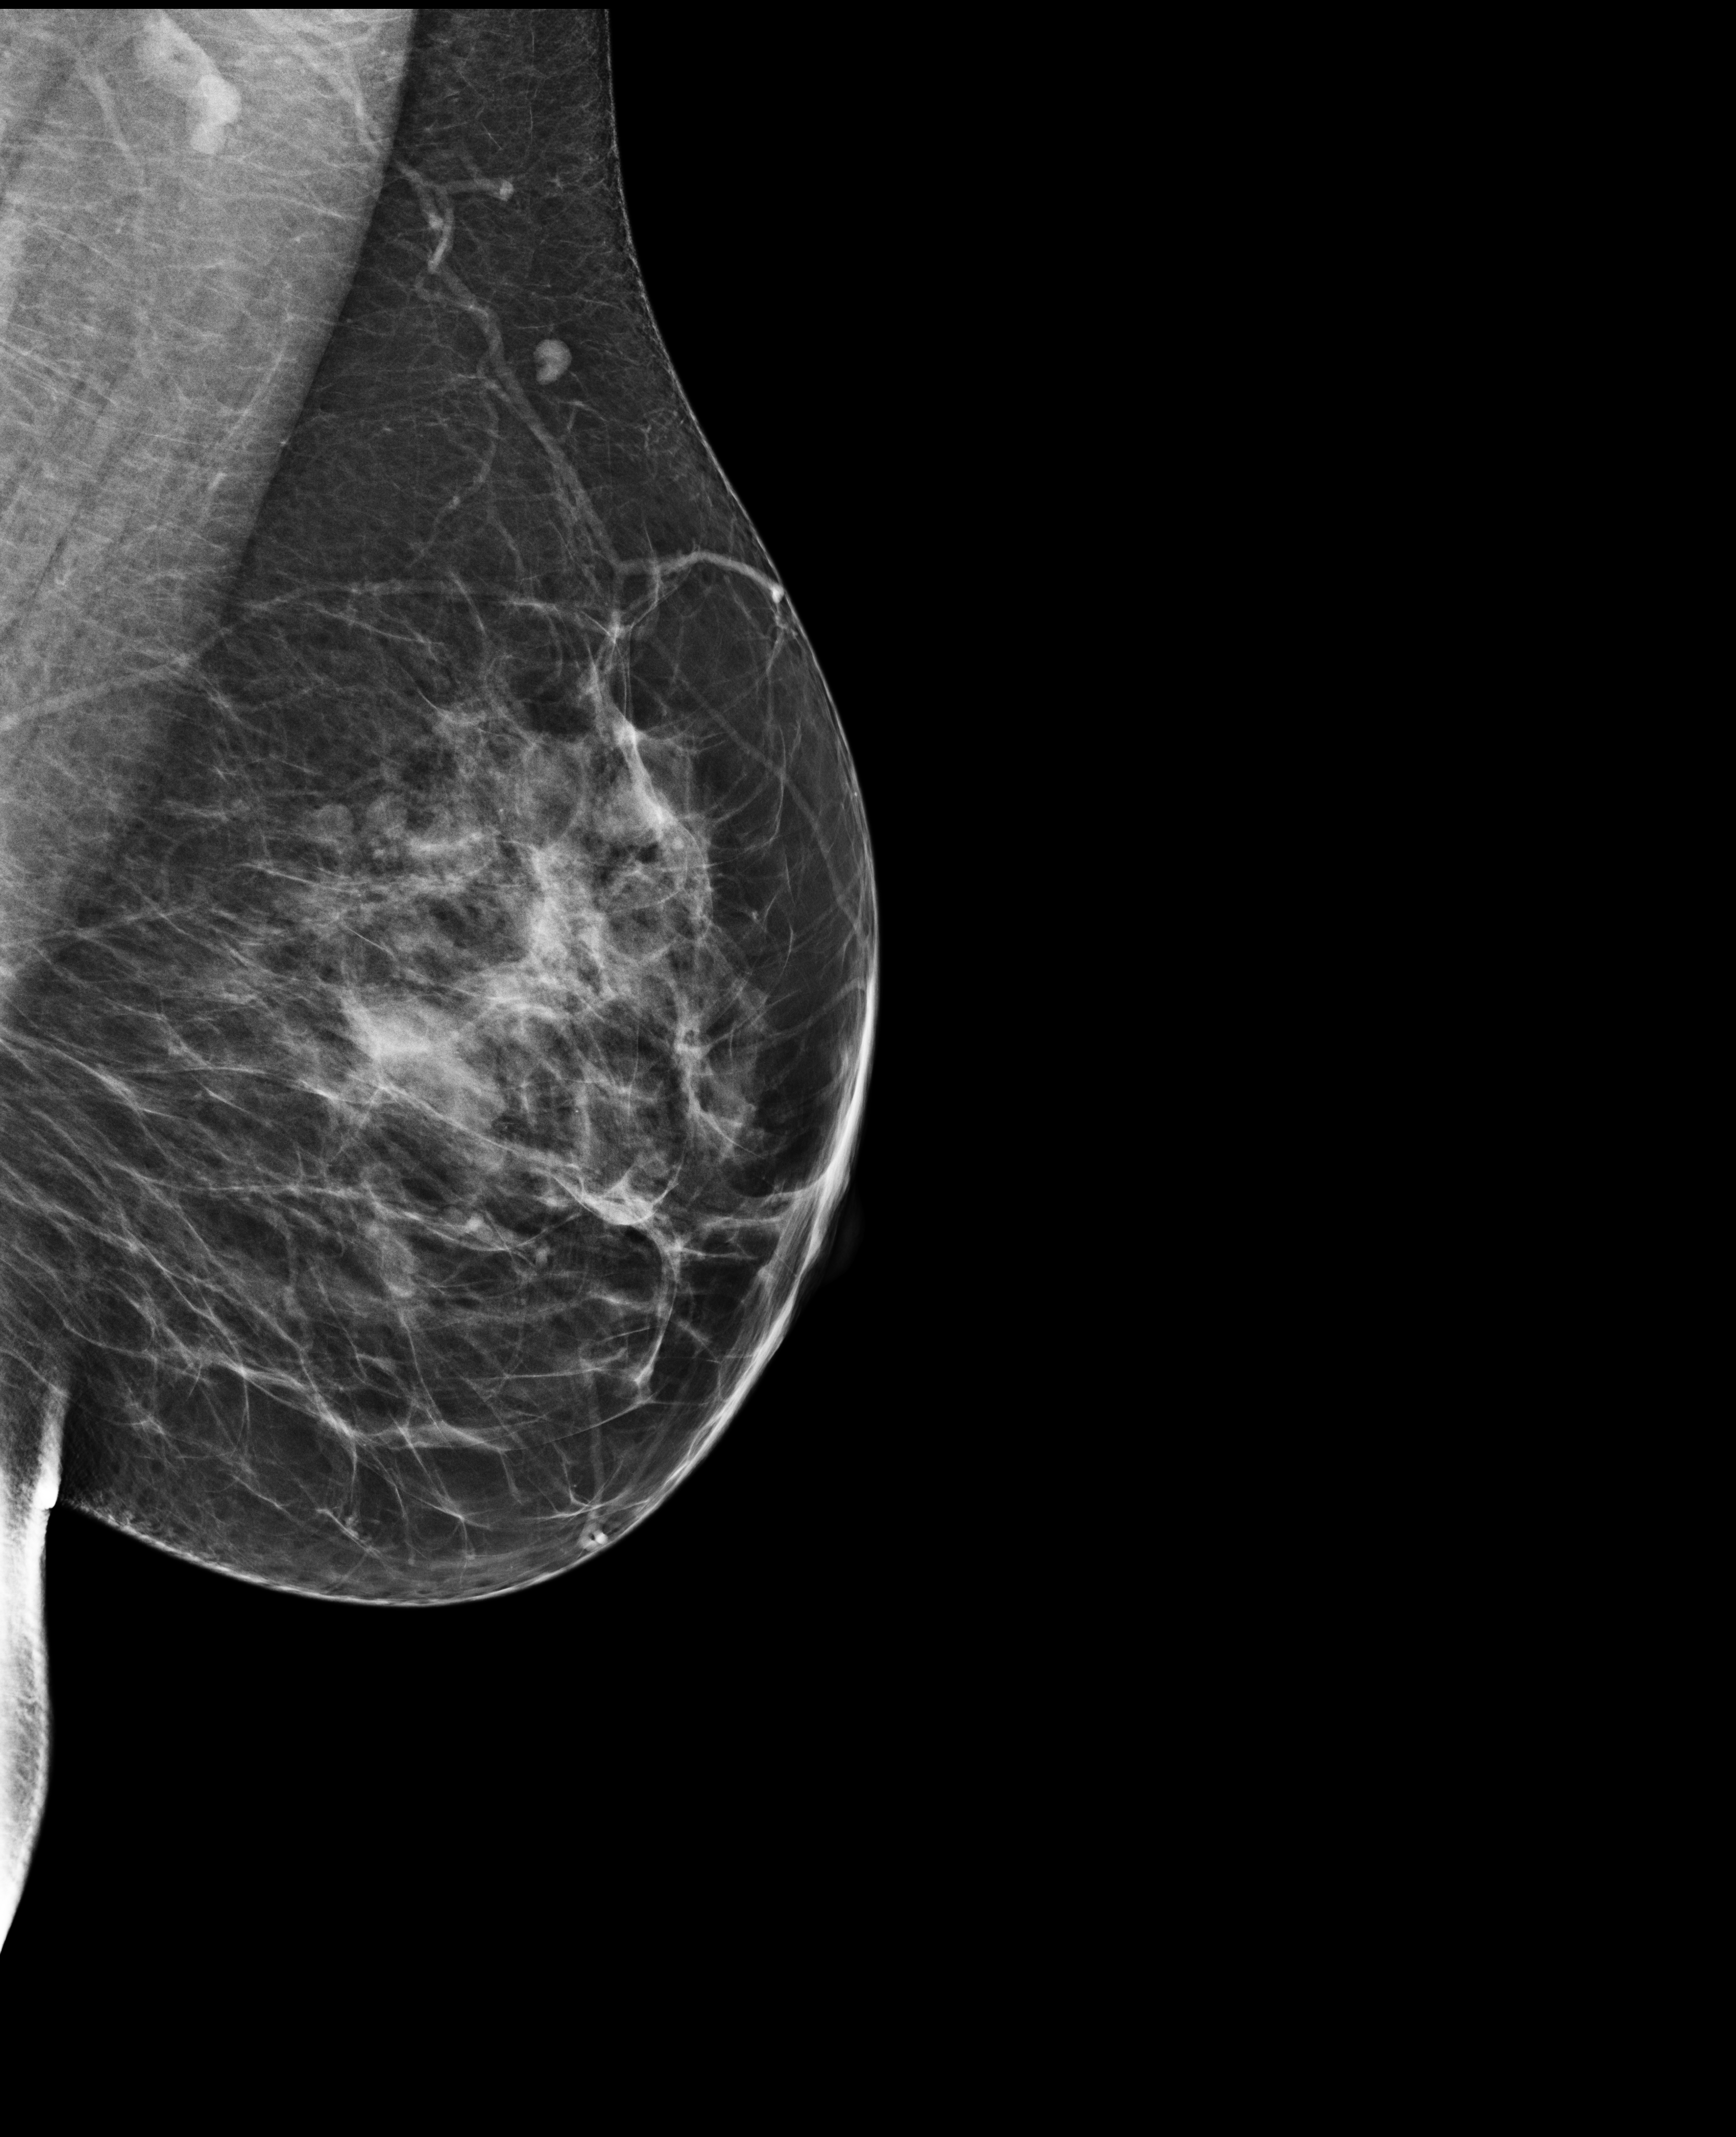
Full-field digital mammogram (FFDM); left breast; mediolateral oblique (MLO) view; annual screening mammography examination; compressed breast thickness 71 mm; system: Selenia Dimensions. Patient aged 44 years (female).
- BI-RADS breast density category at the screening exam (both breasts, scale 1–4): 3
- final BI-RADS assessment for this screening round (tomosynthesis exam, both breasts): category 2
- recall: recalled for additional imaging after this screen